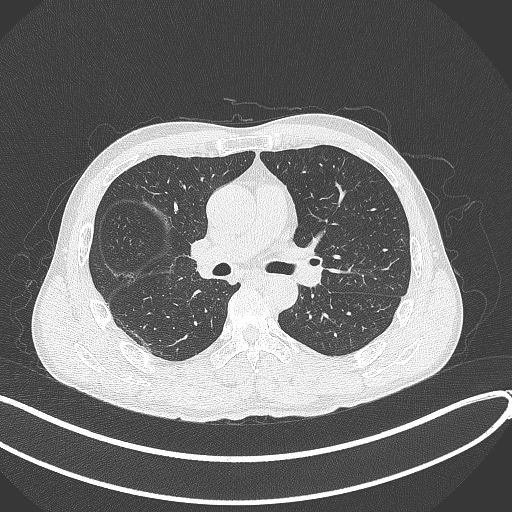
Chest CT, one axial slice. Position 224 of 409 along the scan axis. Lung window (W 1500 / L -600 HU). 512 × 512 image matrix, field of view 400 × 400 mm. Male patient, age 53 years. From the clinical record (not read from this slice): clinical TNM (as recorded): T1b N0 M0.
Annotated regions visible in this slice (rectangle marked by the reading radiologist):
- lung tumour (recorded histology: squamous cell carcinoma): box from (x=186, y=229) to (x=227, y=278) px